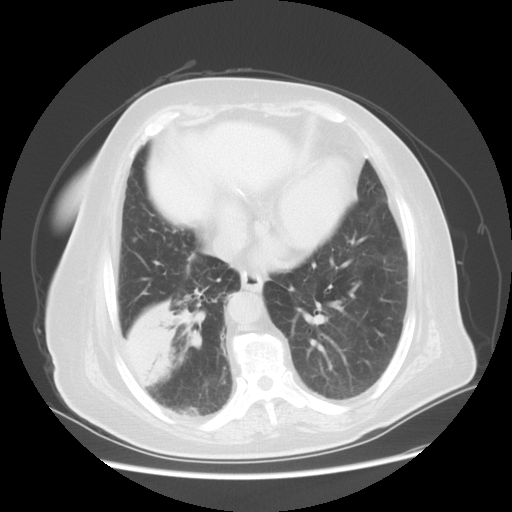
Chest CT, one axial slice. Position 20 of 56 along the scan axis. Reconstruction kernel STANDARD. 120 kVp. Lung window (W 1500 / L -600 HU). 5 mm slice thickness. 512 × 512 image matrix, field of view 378 × 378 mm. Female patient, age 73 years. Case-level facts recorded for this patient, not image findings: clinical TNM (as recorded): T3 N0 M0.
Structures marked on this image (rectangle marked by the reading radiologist):
- lung tumour (recorded histology: adenocarcinoma): bounding box [x1, y1, x2, y2] px = [115, 291, 204, 389]